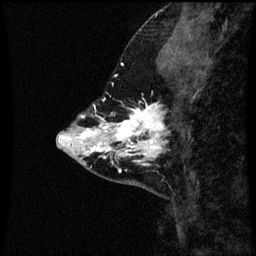
Breast MRI (dynamic contrast-enhanced), one sagittal slice; position 17 of 60 along the scan axis; dynamic contrast-enhanced series, image 2 of 3 at this slice position (ordered by acquisition); 1.5 T; TE 4.2 ms, TR 8.9 ms; 2 mm slice thickness; 256 × 256 image matrix, field of view 200 × 200 mm. Patient: female, 43 years. From the clinical record (not read from this slice): setting: breast cancer imaged before/during neoadjuvant chemotherapy; receptor status: HR-positive, HER2-negative.
Structures marked on this image (semi-automatic segmentation, software-assisted and operator-edited):
- analysis volume of interest (the breast-tissue region the enhancement analysis was run in; not a lesion): box from (x=110, y=104) to (x=168, y=163) px
- tumour enhancement mask (voxels above the 70 % enhancement threshold inside the analysis volume of interest): (x=110, y=104)–(x=165, y=163)